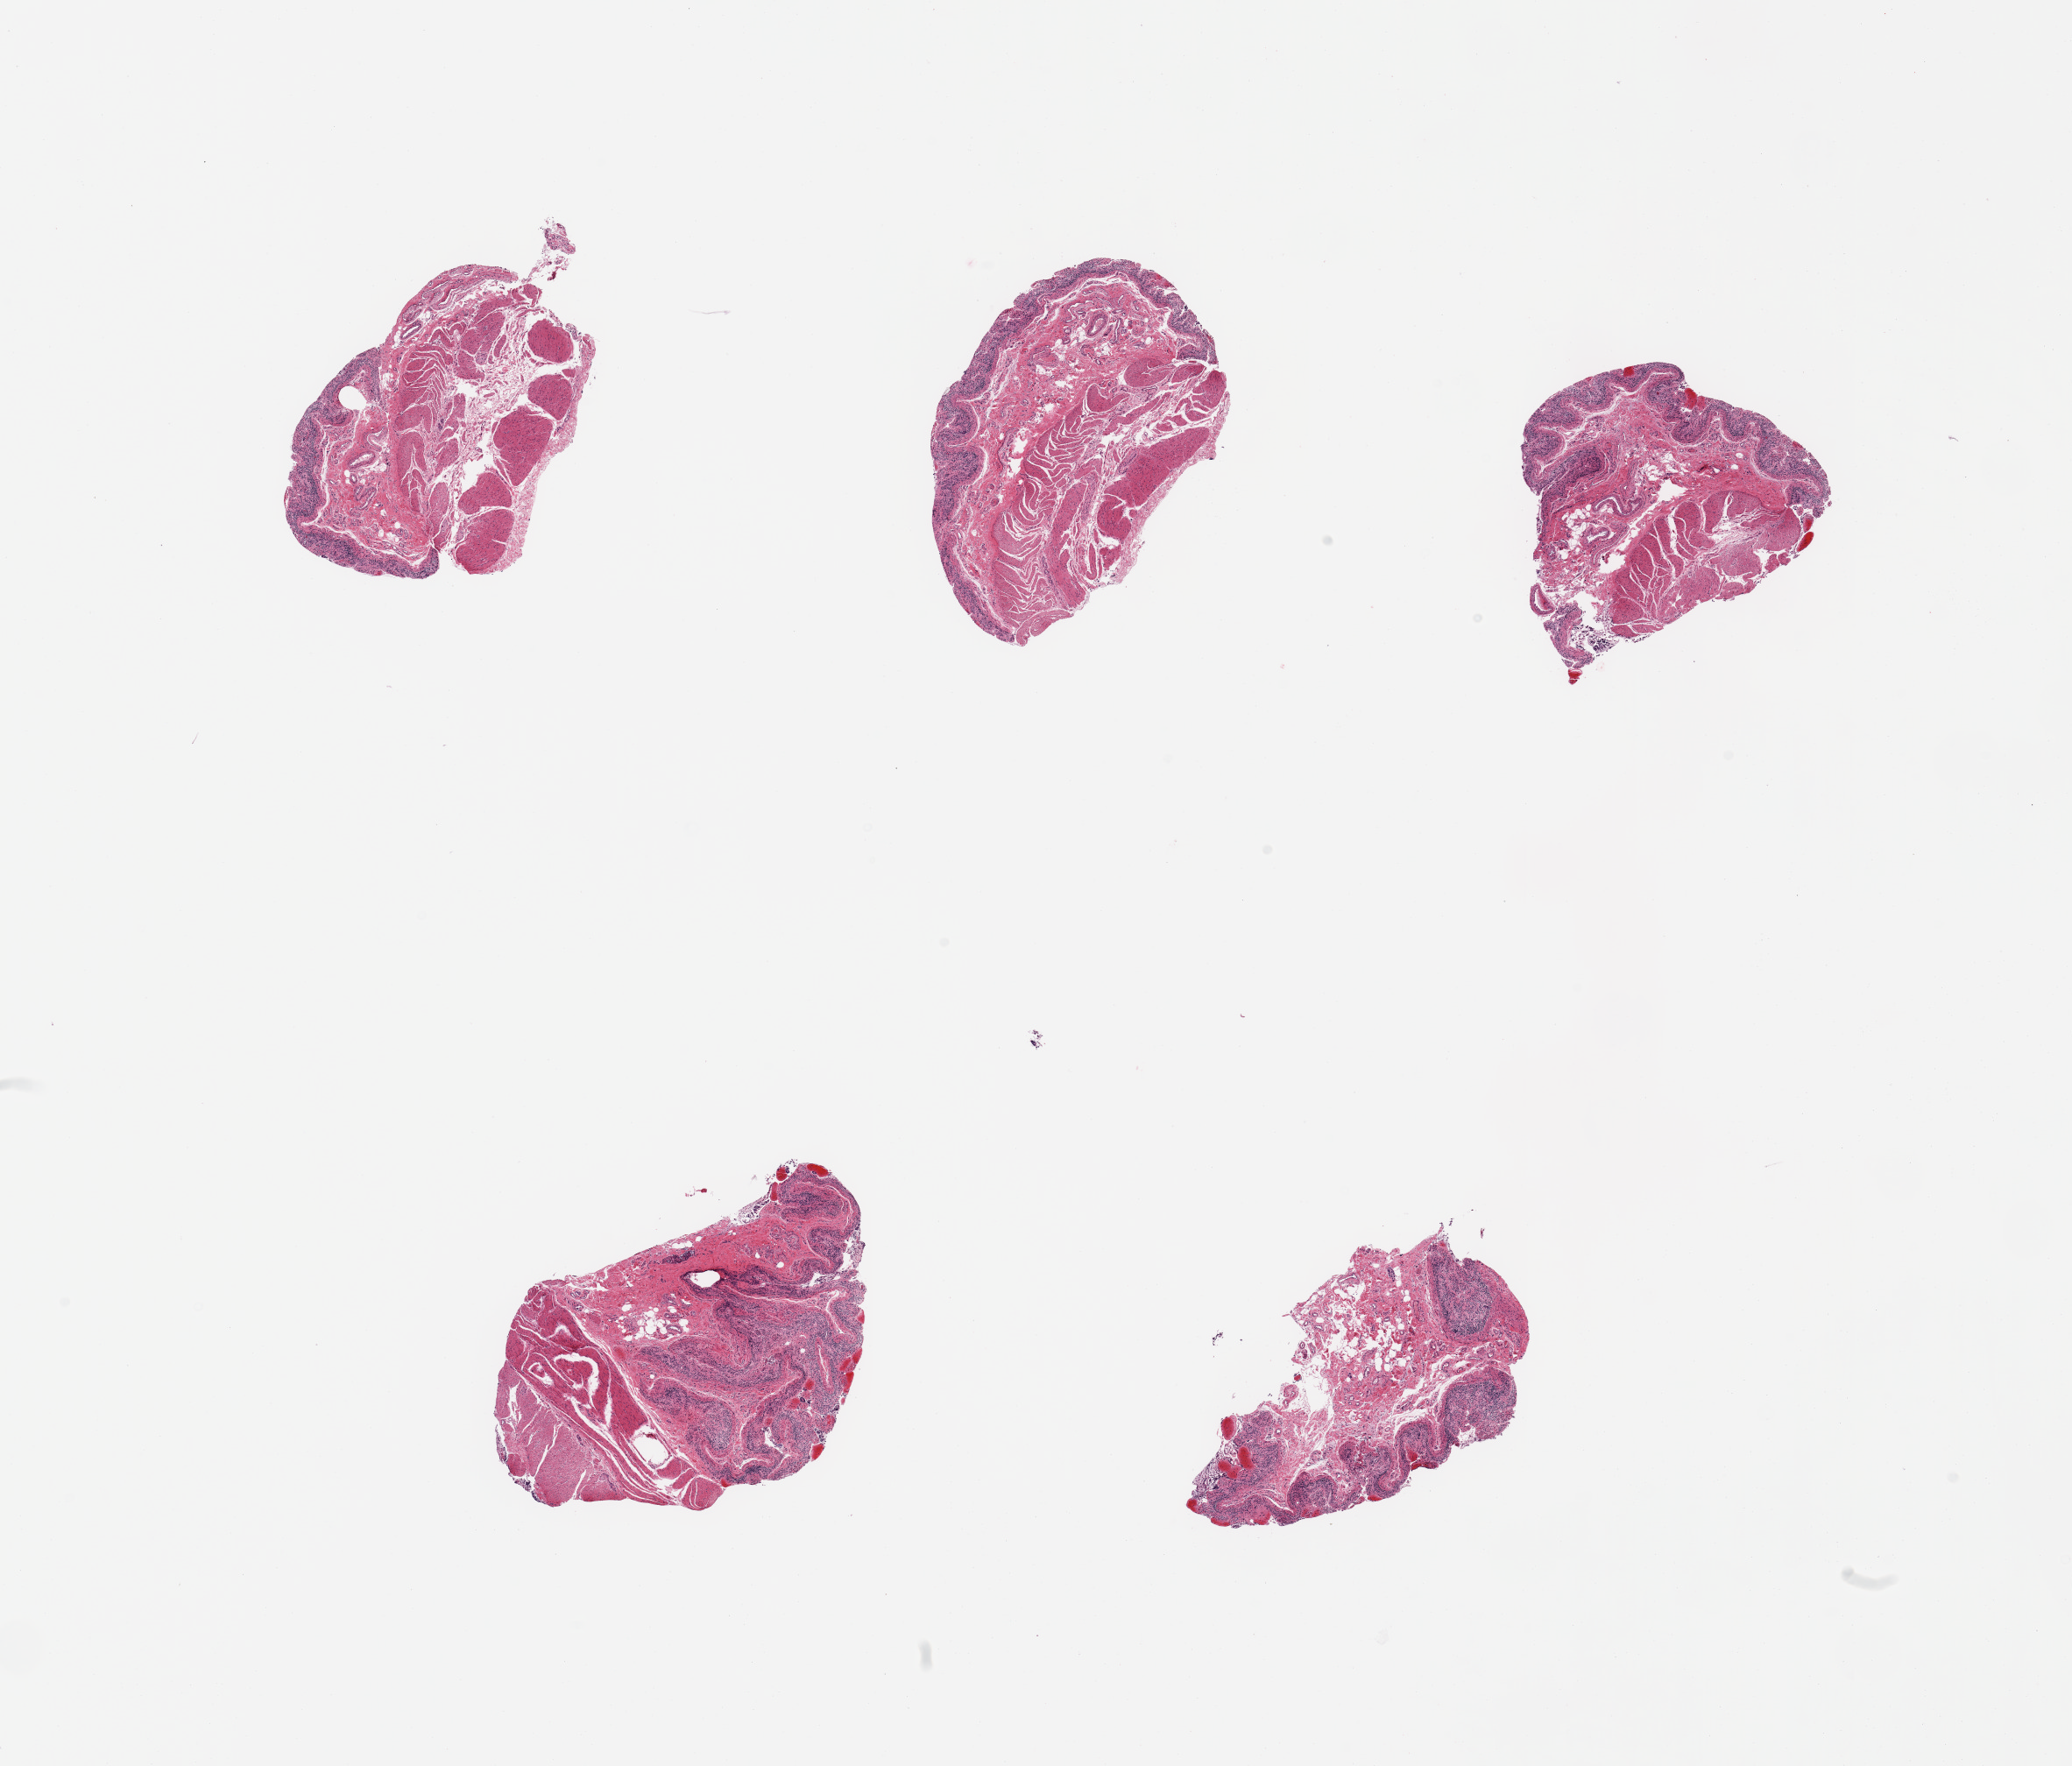
Whole-slide image, H&E stain, brightfield — shown as a low-resolution overview of the whole scanned area (about 18.7 x 15.9 mm). PAXgene-fixed paraffin-embedded (PFPE) section. Sampled site (target tissue): ileum. Donor tissue sample.
• review note (as recorded): 5 pieces; mucosa autolyzed; dispersed lymphoid tissue; muscularis present in 4 pieces